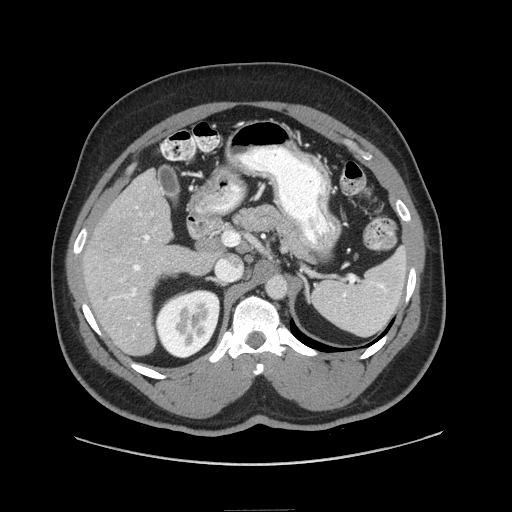
Contrast-enhanced abdominal CT (liver protocol), one axial slice; position 41 of 87 along the scan axis; 140 kVp; soft-tissue window (W 400 / L 40 HU); 2.5 mm slice thickness; 512 × 512 image matrix, field of view 440 × 440 mm. Case-level facts recorded for this patient, not image findings: diagnosis: hepatocellular carcinoma (patient treated with transarterial chemoembolisation; whether this scan precedes or follows treatment is not stated here); TNM stage (as recorded): Stage-II; Child-Pugh class: A; tumour differentiation: moderately differentiated; tumour nodularity: uninodular.
Annotated regions visible in this slice (semi-automatically segmented with operator editing):
- liver parenchyma outside the tumour (the mass and vessels are separate outlines, so this box may not span the whole liver): bounding box [x1, y1, x2, y2] px = [82, 168, 218, 354]
- liver vessels: [110, 187, 153, 325]